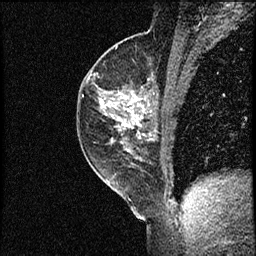
Breast MRI (dynamic contrast-enhanced), one sagittal slice; slice 35 of 56 in the series (ordered by position); dynamic contrast-enhanced study with each time point stored as its own series, time point 2 of 3 at this slice position (early post-contrast, ordered by acquisition time); 1.5 T; TE 4.2 ms, TR 17.3 ms; 2 mm slice thickness; 256 × 256 image matrix, field of view 200 × 200 mm. Female patient. From the clinical record (not read from this slice): setting: breast cancer imaged before/during neoadjuvant chemotherapy; receptor status: HER2-positive.
Annotated regions visible in this slice (semi-automatic segmentation, software-assisted and operator-edited):
- analysis volume of interest (the breast-tissue region the enhancement analysis was run in; not a lesion): bounding box (x1, y1, x2, y2) in pixels: (77, 50, 156, 155)
- tumour enhancement mask (voxels above the 100 % enhancement threshold inside the analysis volume of interest): (101, 91, 149, 129)